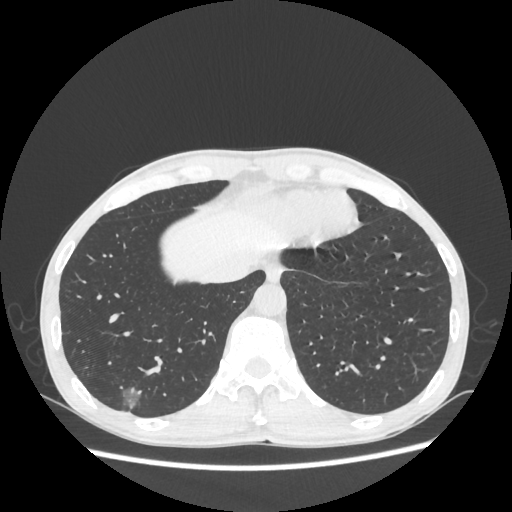
Chest CT, one axial slice. Slice 65 of 270 in the series (ordered by position). Lung window (W 1500 / L -600 HU). 1.25 mm slice thickness. 512 × 512 image matrix, field of view 360 × 360 mm. Patient: male, 60 years. From the clinical record (not read from this slice): clinical TNM (as recorded): T1c N0 M0; histopathological grade: G2.
Outlined on this slice (bounding box drawn by a radiologist):
- lung tumour (recorded histology: adenocarcinoma): bounding box [x1, y1, x2, y2] px = [117, 380, 148, 417]